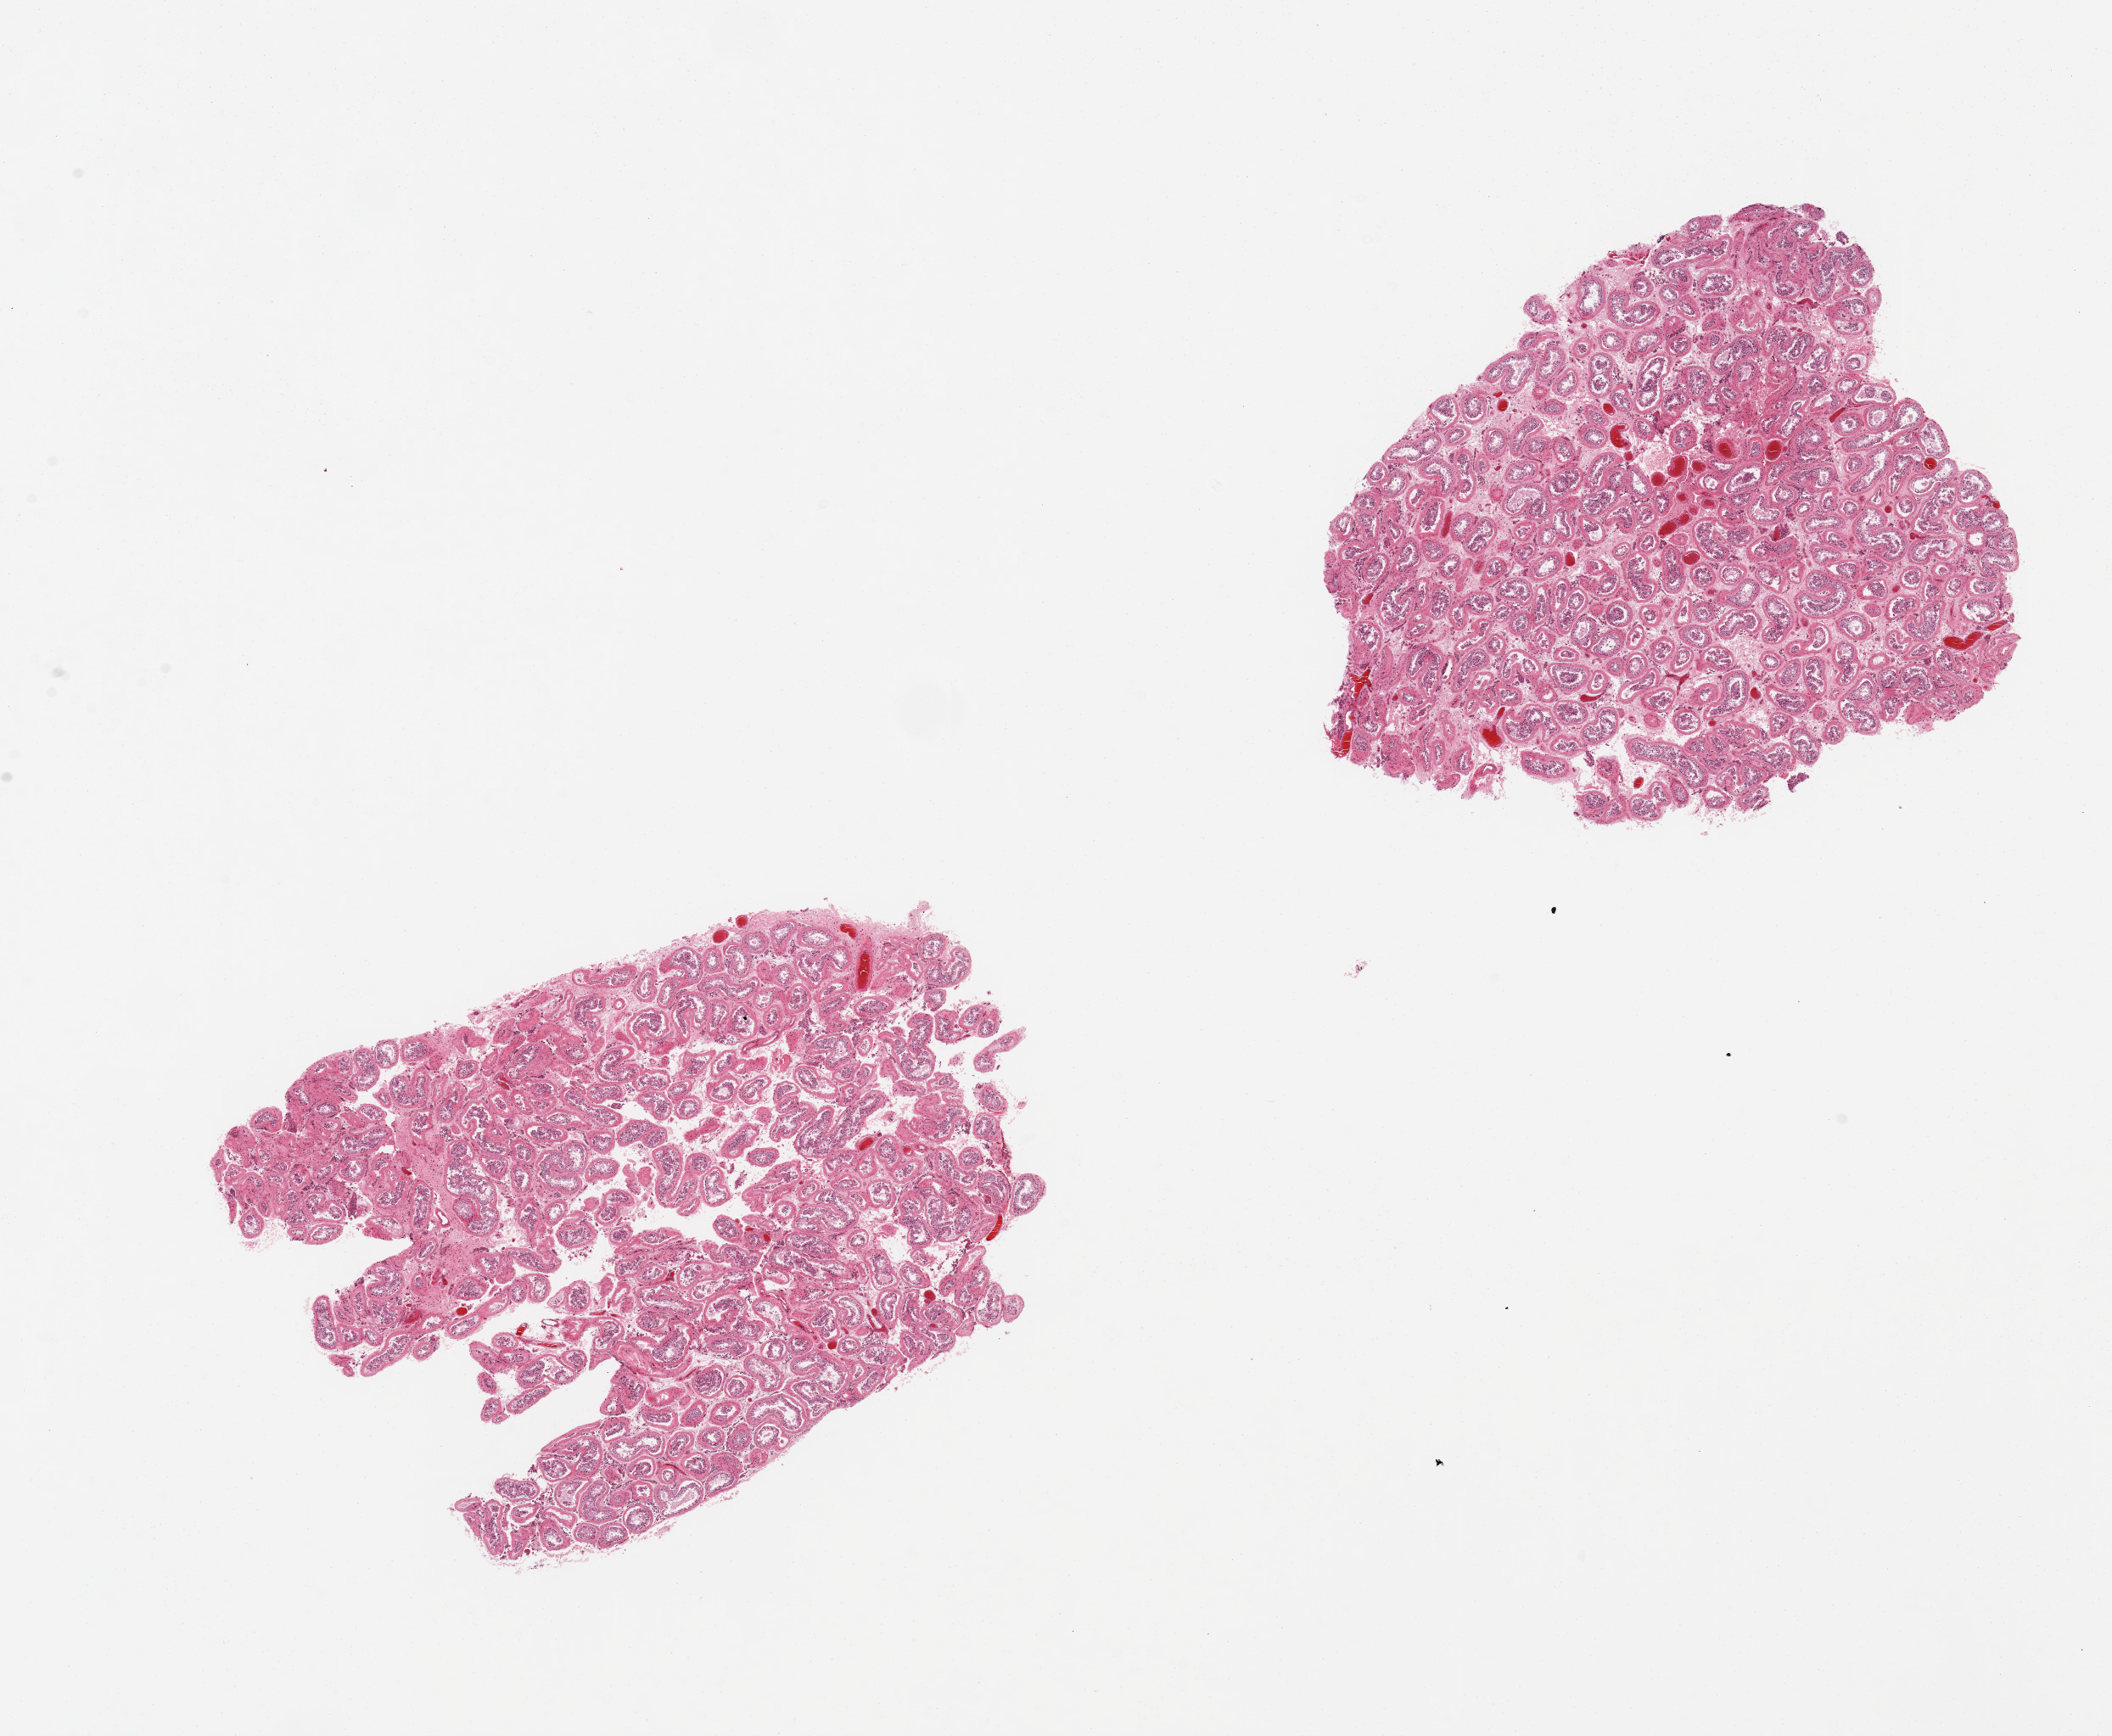
Digitized H&E-stained section, brightfield — shown as a low-resolution overview of the whole scanned area (about 19.7 x 16.2 mm); PAXgene-fixed, paraffin-embedded tissue; target tissue: testis; tissue donor sample.
Review note (as recorded): 2 pieces. markedly diminished spermatogenesis.